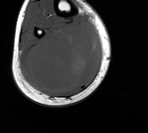
MRI of an extremity soft-tissue mass, one axial slice. Slice 49 of 76 in the series (ordered by position). MR volume resampled by the dataset authors to the PET/CT grid (not the native acquisition matrix). 3.27 mm slice thickness. 148 × 133 image matrix, field of view 145 × 130 mm. Male patient. From the clinical record (not read from this slice): histological type: liposarcoma - round cell; grade: high; site of the primary tumour: right calf.
Structures marked on this image (expert contour drawn on MRI and transferred to this co-registered scan by the dataset authors):
- gross tumour volume (mass): box from (x=24, y=23) to (x=101, y=93) px